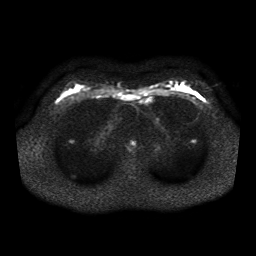
Breast MRI, one axial slice. Position 25 of 41 along the scan axis. Diffusion-weighted series; image 2 of 4 stored at this slice position (different b-values; order by instance number). 1.5 T. 5 mm slice thickness. 256 × 256 image matrix. Female patient.
Outlined on this slice (manually delineated by an expert):
- tumour on diffusion-weighted imaging: bounding box (x1, y1, x2, y2) in pixels: (194, 93, 201, 98)